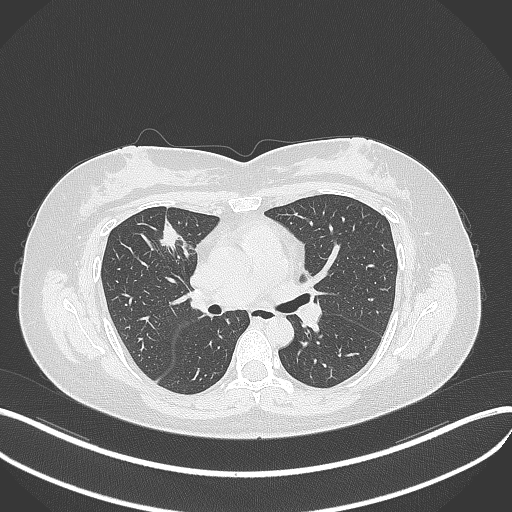
Chest CT, one axial slice. Slice 184 of 273 in the series (ordered by position). Reconstruction kernel B70f. Lung window (W 1500 / L -600 HU). 1 mm slice thickness. 512 × 512 image matrix. Female patient, age 42 years. Case-level facts recorded for this patient, not image findings: clinical TNM (as recorded): T1b N0 M0.
Annotated regions visible in this slice (bounding box drawn by a radiologist):
- lung tumour (recorded histology: adenocarcinoma): bounding box [x1, y1, x2, y2] px = [156, 218, 183, 253]